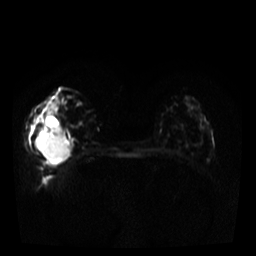
Breast MRI, one axial slice; slice 13 of 34 in the series (ordered by position); diffusion-weighted series; image 2 of 4 stored at this slice position (different b-values; order by instance number); 3 T; 5 mm slice thickness; 256 × 256 image matrix, field of view 320 × 320 mm. Female patient.
Outlined on this slice (expert manual segmentation):
- tumour on diffusion-weighted imaging: bounding box (x1, y1, x2, y2) in pixels: (37, 129, 70, 163)